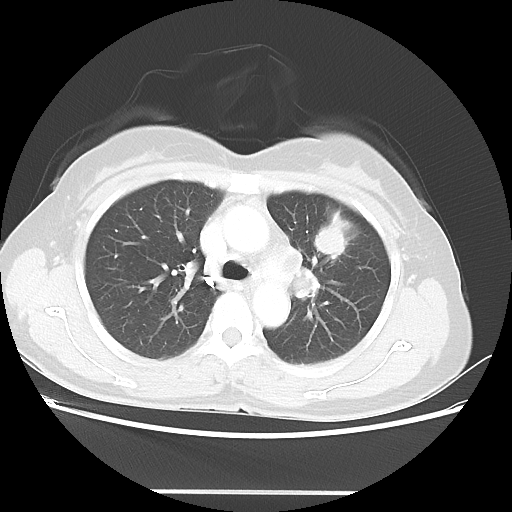
Chest CT, one axial slice. Slice 31 of 46 in the series (ordered by position). Reconstruction kernel LUNG. 100 kVp. Lung window (W 1500 / L -600 HU). 512 × 512 image matrix, field of view 360 × 360 mm. Female patient, age 50 years. From the clinical record (not read from this slice): clinical TNM (as recorded): T1c N1 M0; histopathological grade: G3.
Outlined on this slice (bounding box drawn by a radiologist):
- lung tumour (recorded histology: adenocarcinoma): bounding box [x1, y1, x2, y2] px = [313, 209, 348, 258]